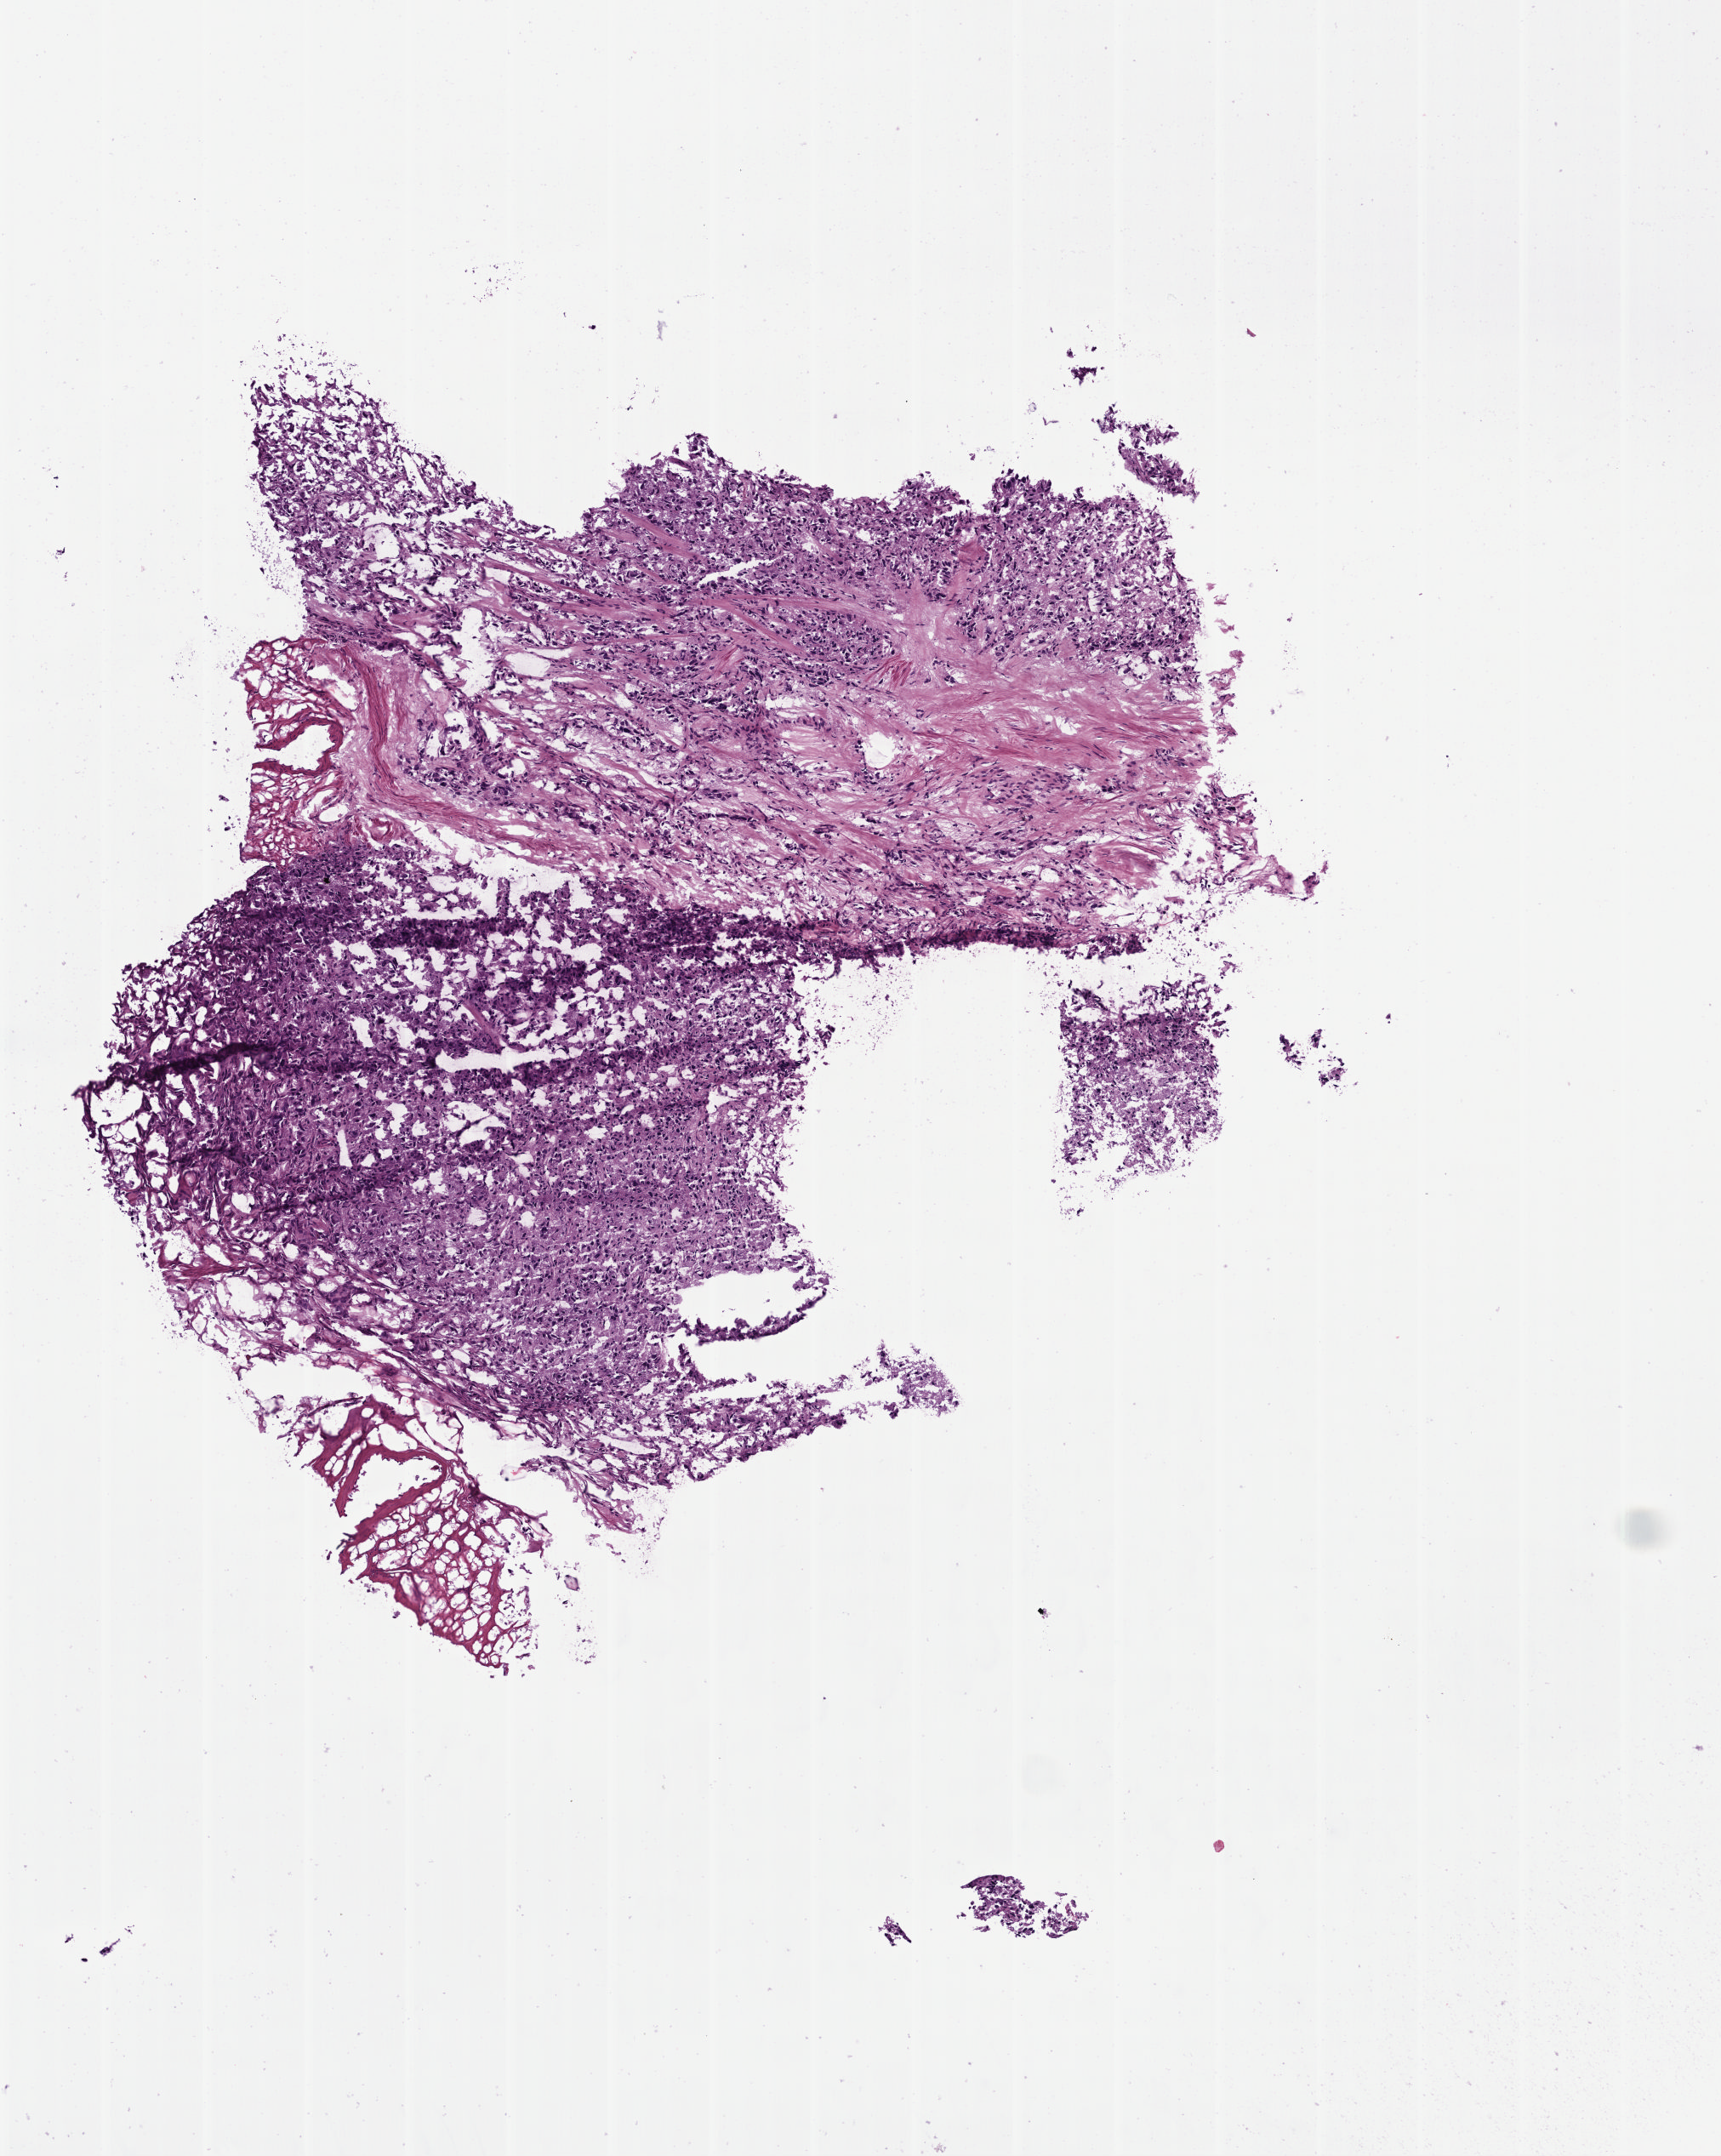
H&E whole-slide image — shown as a low-resolution overview of the whole scanned area (about 4.0 x 5.0 mm, slide scanned at 40x). Frozen section from the top of the tissue portion. Adrenal gland, primary tumour sample. Female, age 35 years at initial diagnosis. Slide review estimates, as recorded: tumour cells 75%, tumour nuclei 75%, normal cells 0%, stromal cells 25%, necrosis 0%. Inflammatory infiltration, as recorded: lymphocyte infiltration 40%, monocyte infiltration 20%, neutrophil infiltration 20%.
Diagnosis: Paraganglioma, malignant.